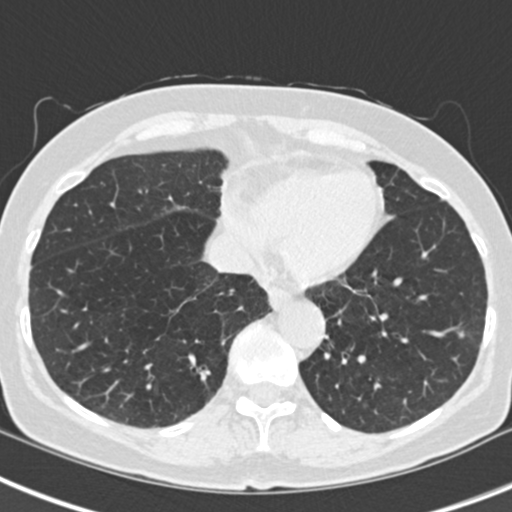
Low-dose screening chest CT, one axial slice. Position 74 of 229 along the scan axis. Reconstruction kernel B30f. Lung window (W 1500 / L -600 HU). 2 mm slice thickness. 512 × 512 image matrix.
Outlined on this slice (manually delineated by an expert):
- lesion 1 (tumor): box from (x=458, y=331) to (x=464, y=338) px